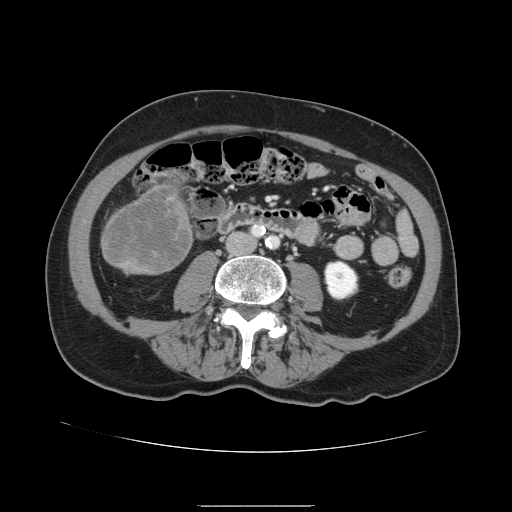
Contrast-enhanced abdominal CT, one axial slice. Position 23 of 168 along the scan axis. Intravenous contrast given. Soft-tissue window (W 400 / L 40 HU). 2.5 mm slice thickness. 512 × 512 image matrix, field of view 386 × 386 mm. Male patient, age 74 years. Case-level facts recorded for this patient, not image findings: diagnosis: colorectal cancer liver metastases, imaged before liver resection; multiple liver metastases: no; largest metastasis: 14.5 cm; disease in both lobes: yes.
Structures marked on this image (manually delineated by an expert):
- liver: bounding box <102,181,193,275> (left, top, right, bottom; pixels)
- liver metastasis: <106,186,190,271>